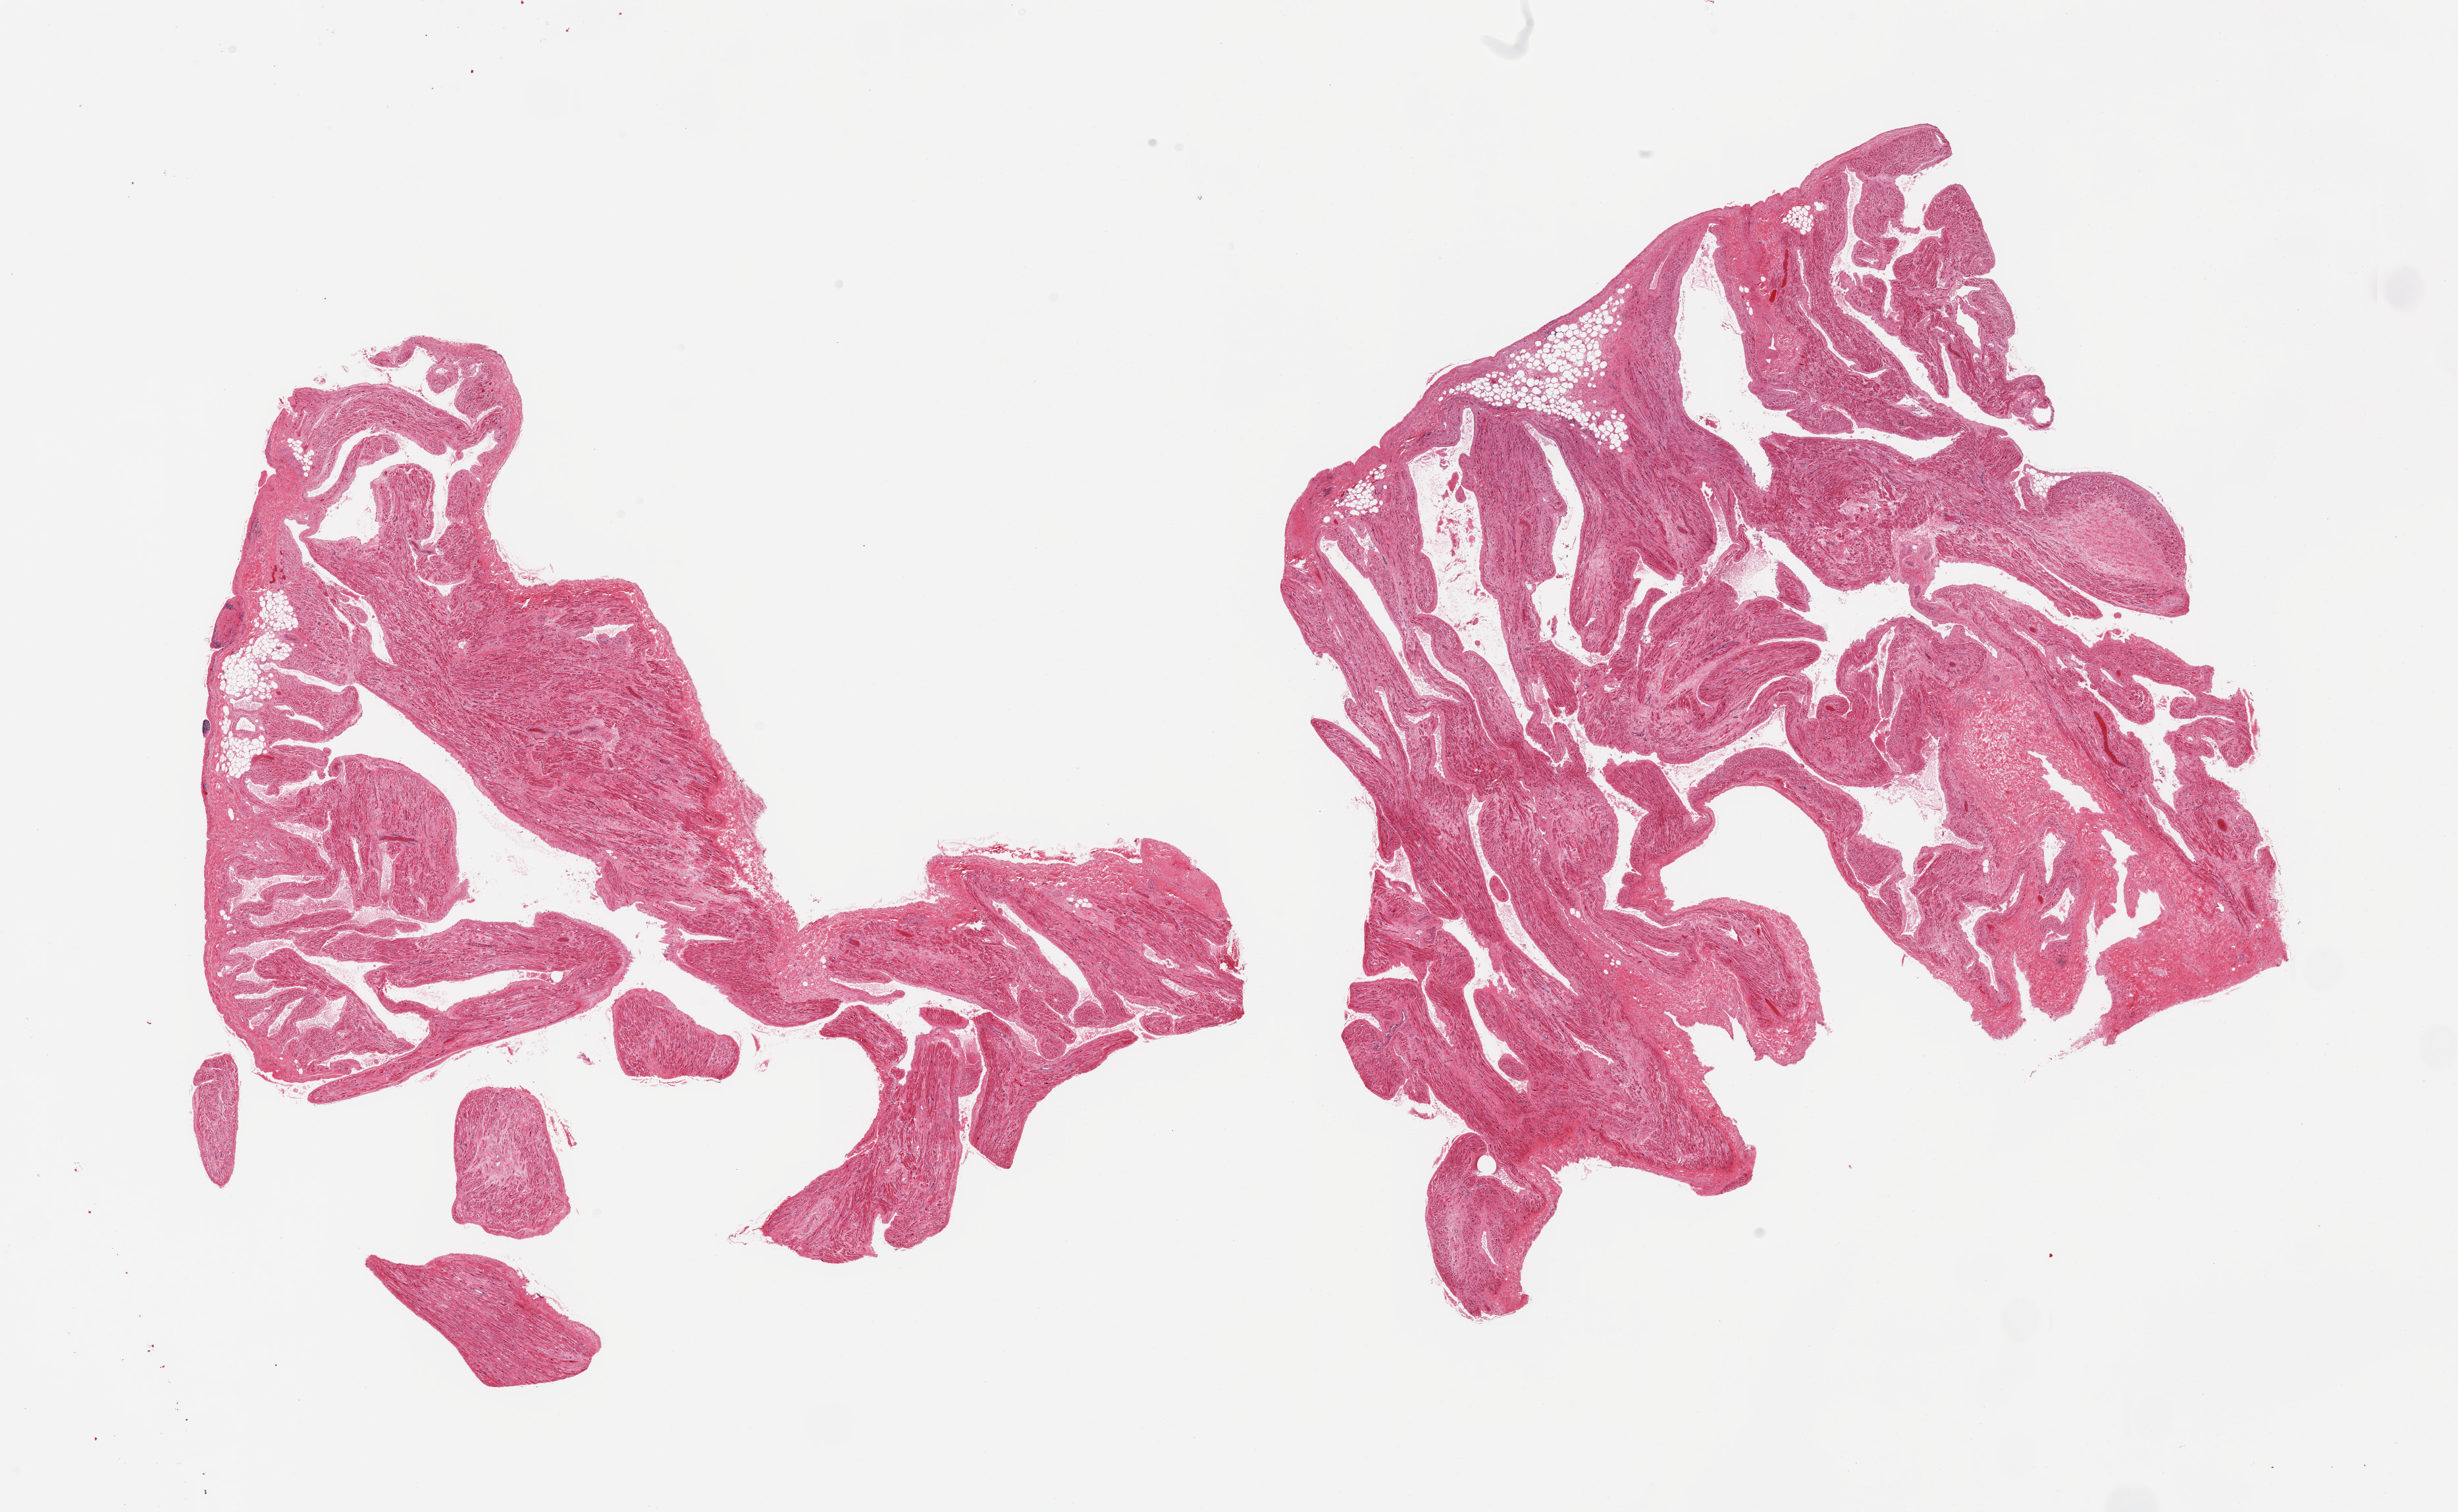
Hematoxylin and eosin (H&E) whole-slide image — whole scanned area (about 29.5 x 18.2 mm, slide scanned at 20x) shown as a low-resolution overview; PAXgene-fixed paraffin-embedded (PFPE) section; sampled site (target tissue): auricular appendage; tissue donor sample.
- review note (as recorded): 2 pieces; myocyte hypertrophy and interstitial fibrosis, ? ischemic change